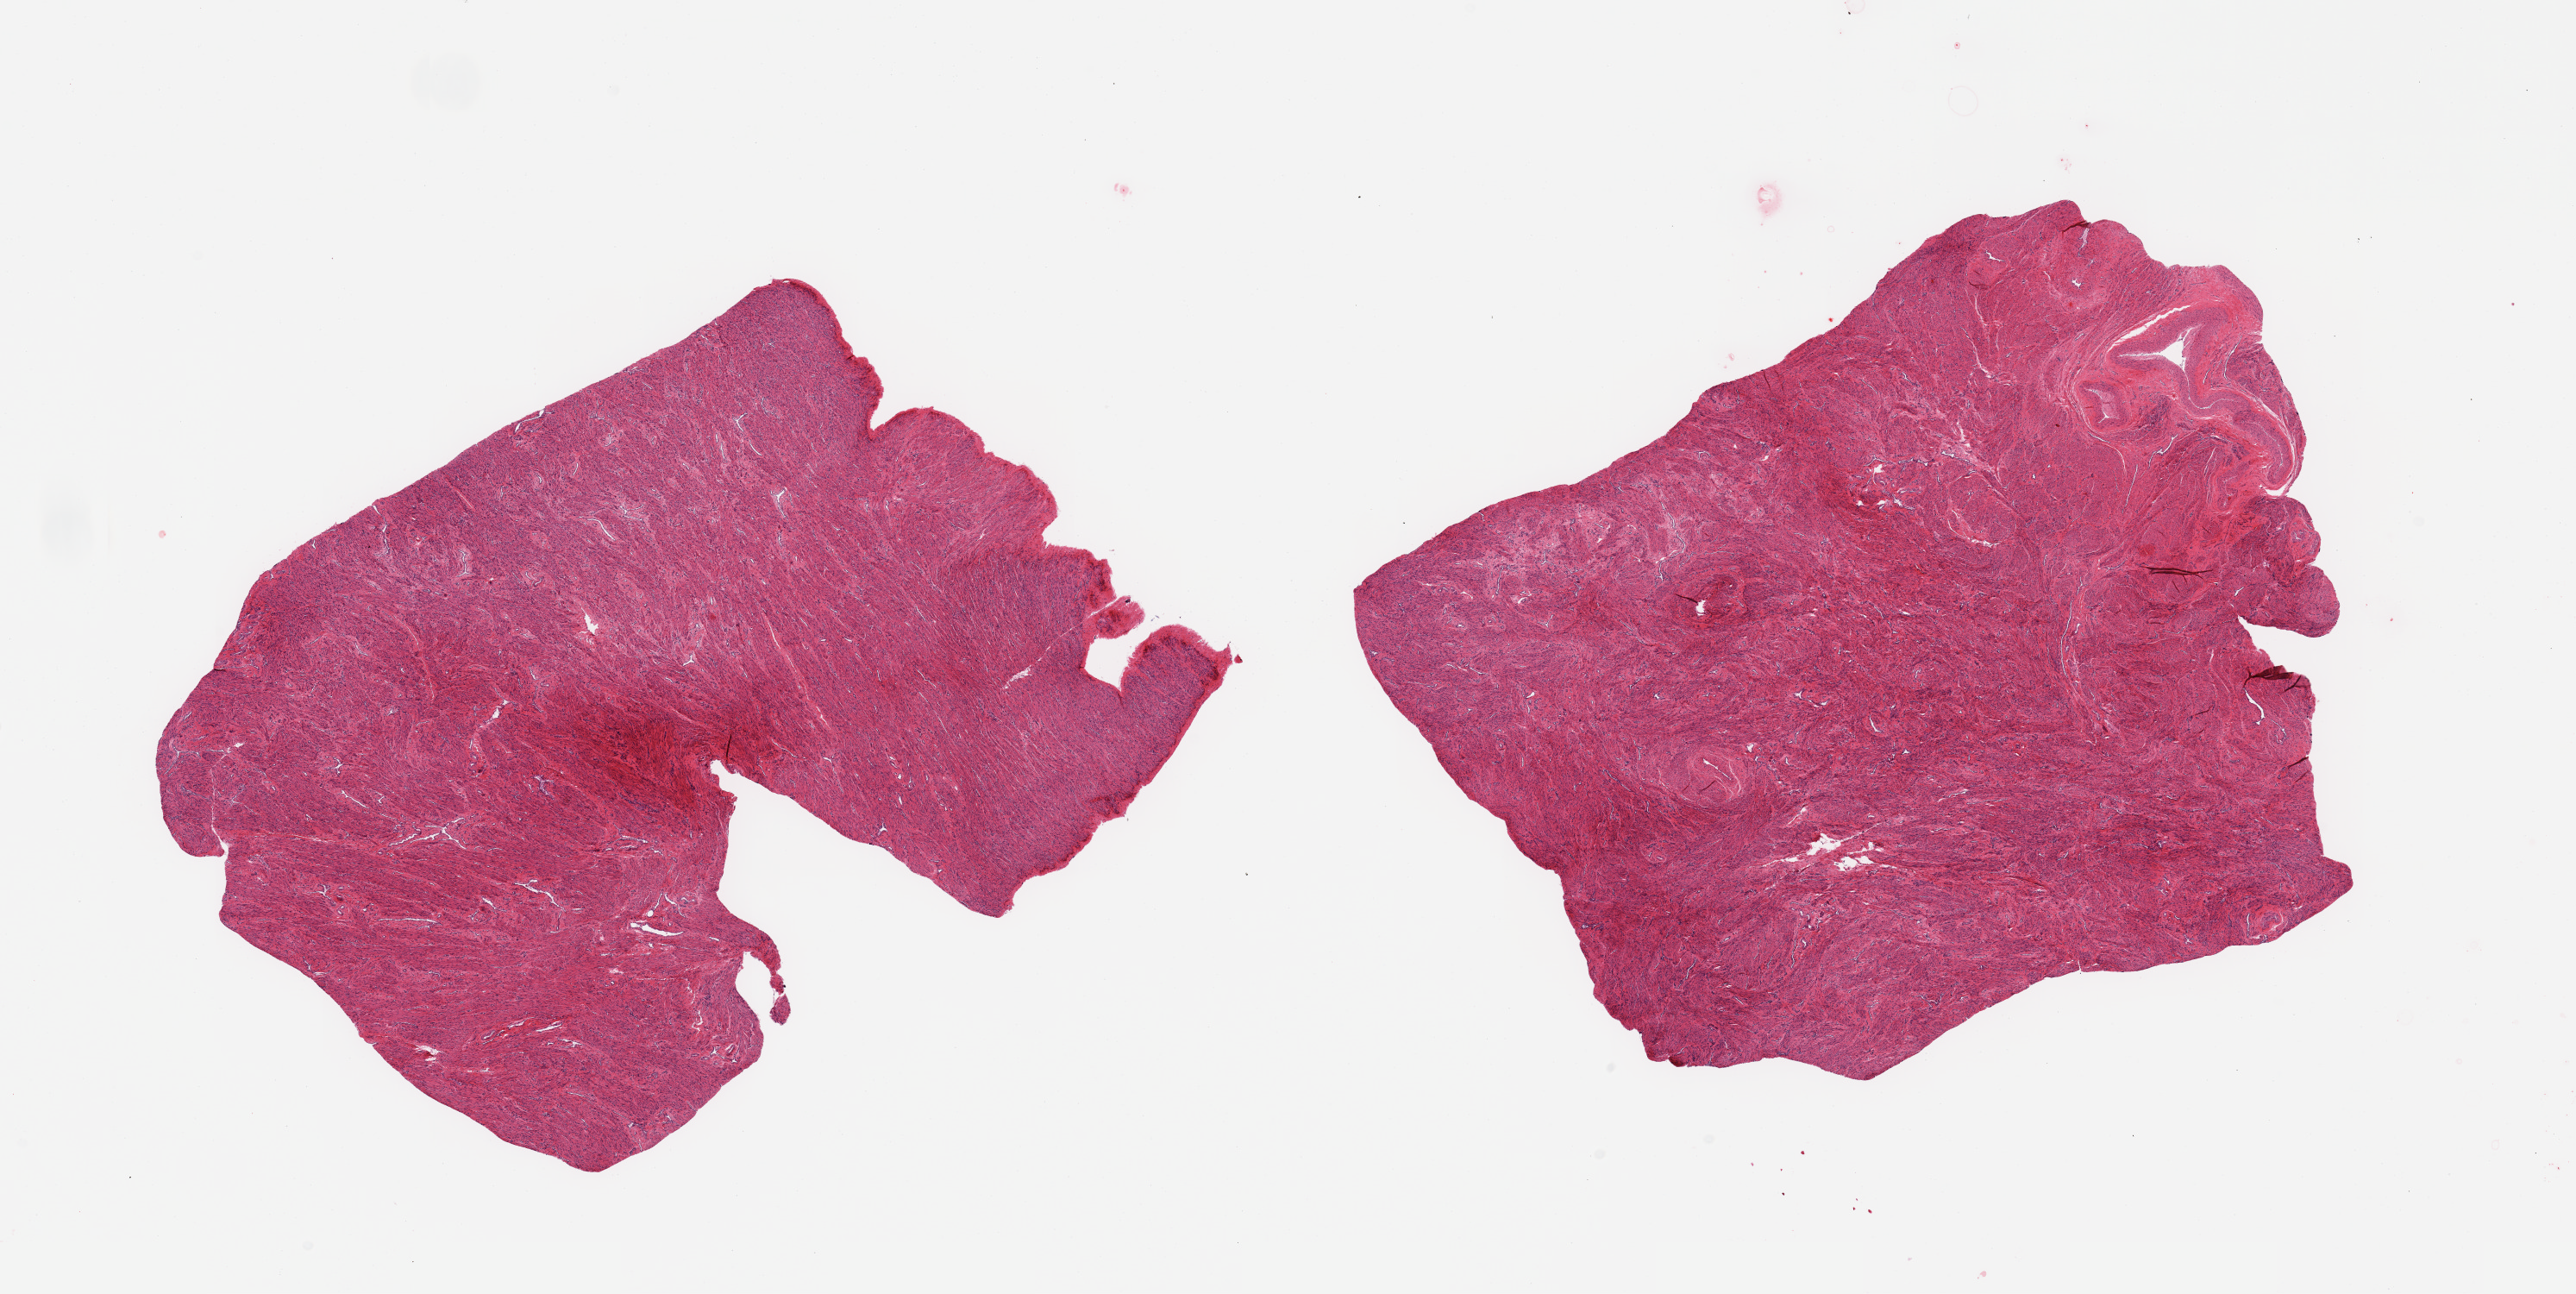
Hematoxylin and eosin (H&E) whole-slide image, a low-resolution overview of the entire scanned area, about 23.6 x 11.9 mm, PAXgene-fixed, paraffin-embedded tissue, sampled site (target tissue): uterus, tissue donor sample. Donor: female.
Review note (as recorded): 2 pieces; only myometrium in these sections, no endometrium.